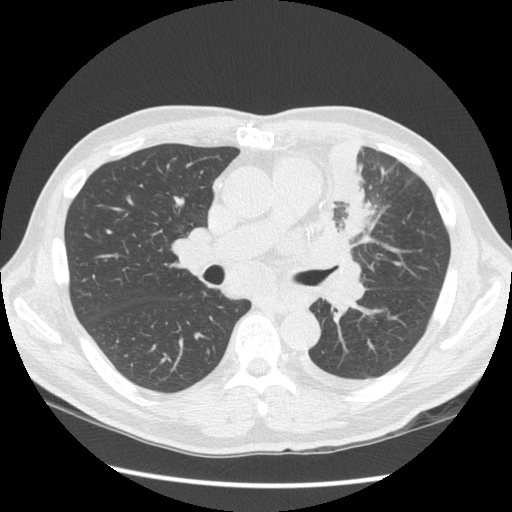
Low-dose screening chest CT, one axial slice. 120 kVp. Lung window (W 1500 / L -600 HU). 2.5 mm slice thickness. 512 × 512 image matrix, field of view 360 × 360 mm.
Structures marked on this image (outlined manually by an expert reader):
- lesion 1 (tumor, upper lobe of left lung): bounding box (x1, y1, x2, y2) in pixels: (304, 143, 373, 269)